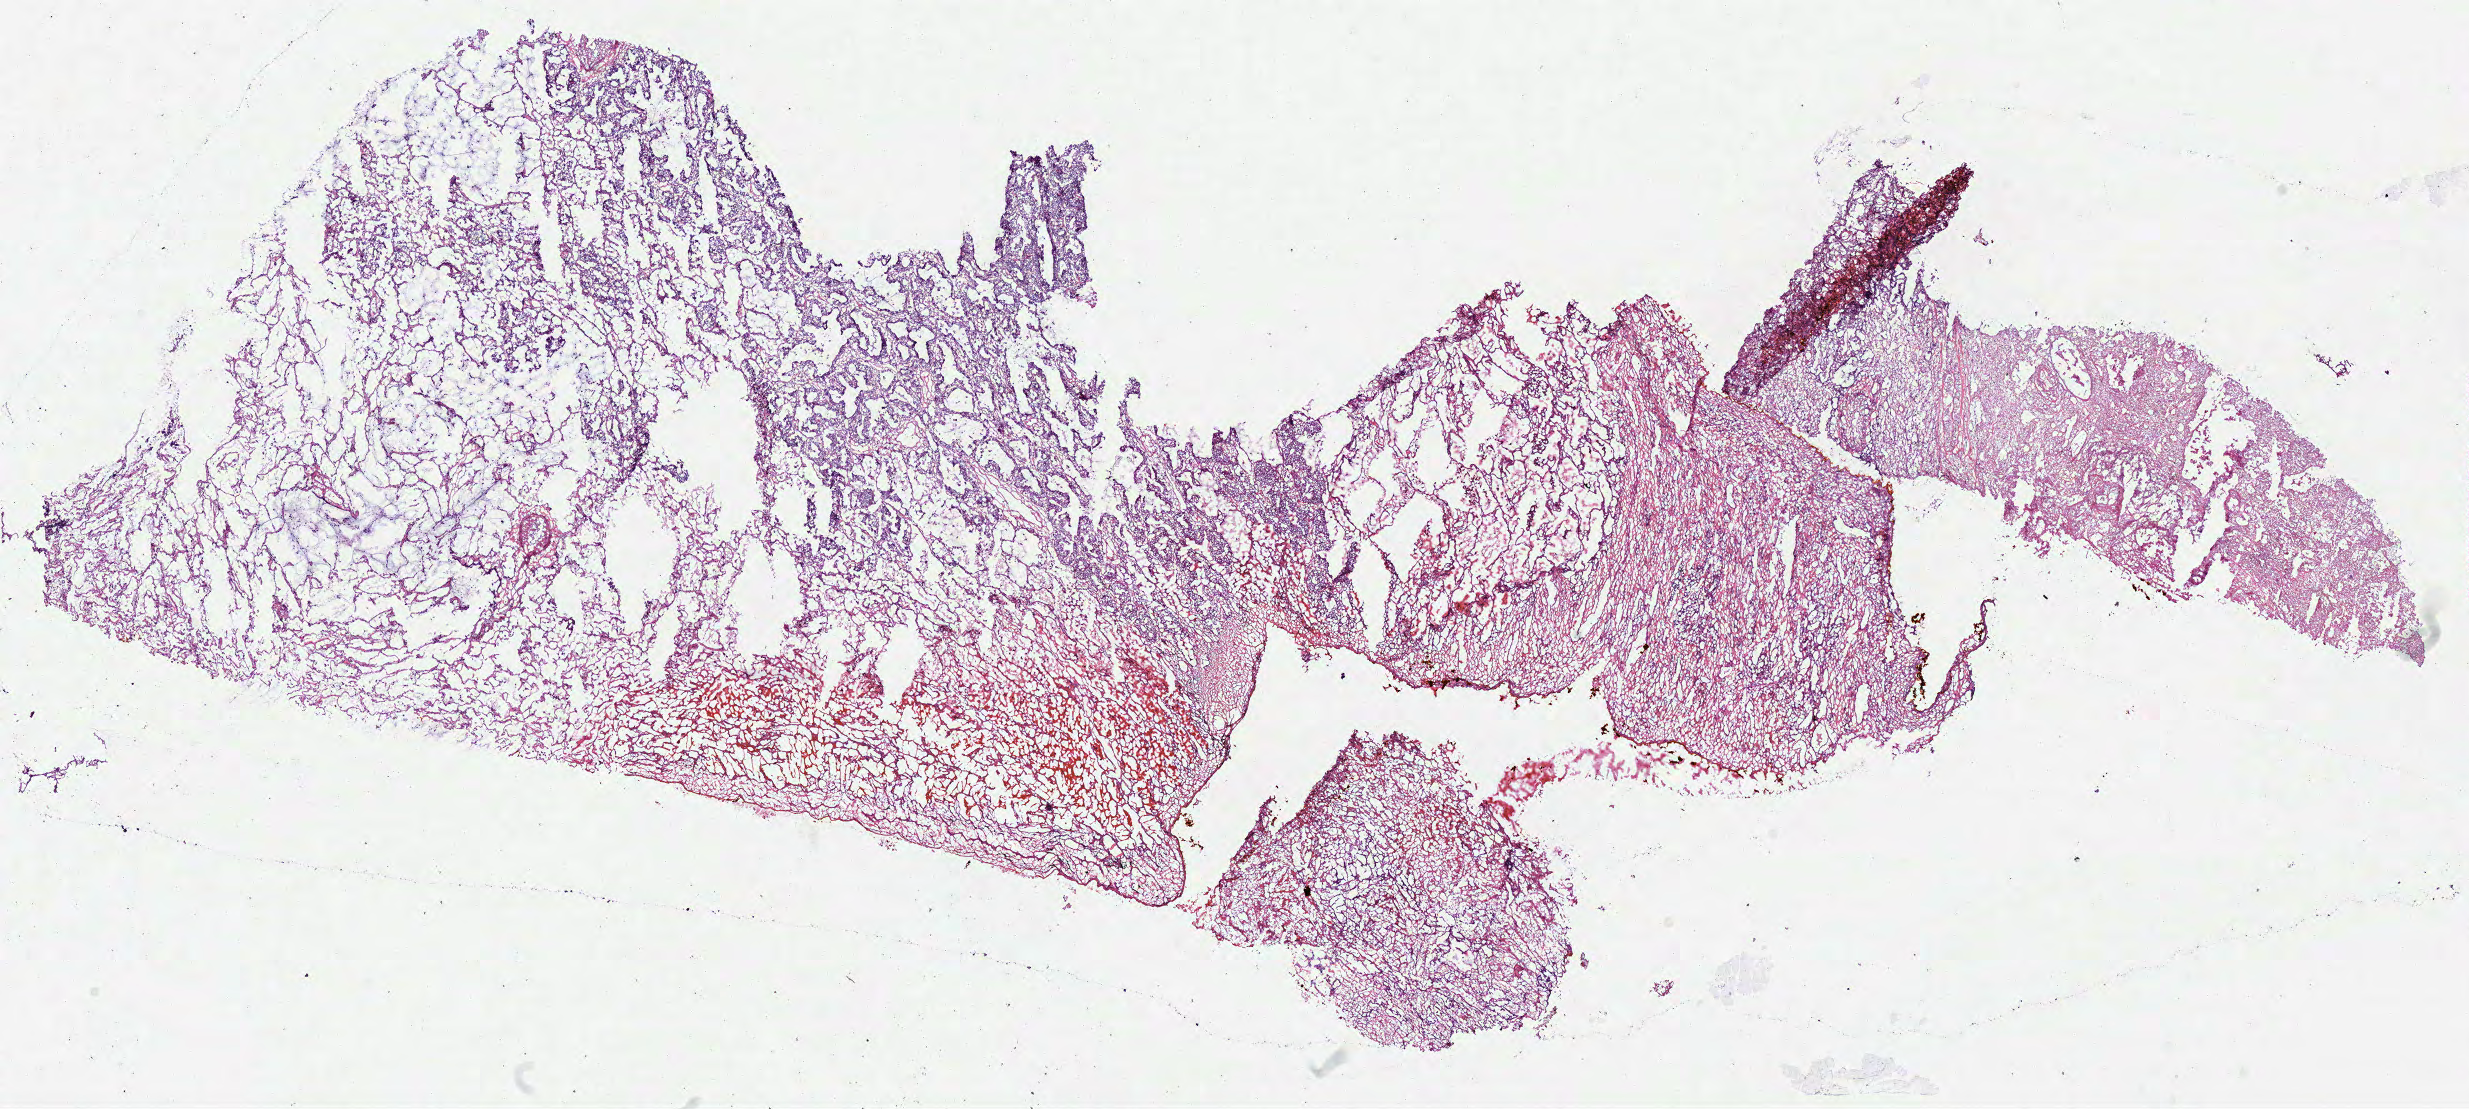
Digitized Hematoxylin and eosin (H&E) stained tissue section (whole slide), a low-resolution overview of the entire scanned area, about 19.5 x 8.7 mm, frozen section from the bottom of the tissue portion, sample: primary tumour, lung. Male, age 70 years at initial diagnosis. Slide review estimates, as recorded: tumour cells 35%, tumour nuclei 50%, normal cells 50%, stromal cells 15%, necrosis 0%.
AJCC pathologic stage: IIA. Laterality: left. Histologic diagnosis: Mucinous adenocarcinoma (upper lobe, lung).